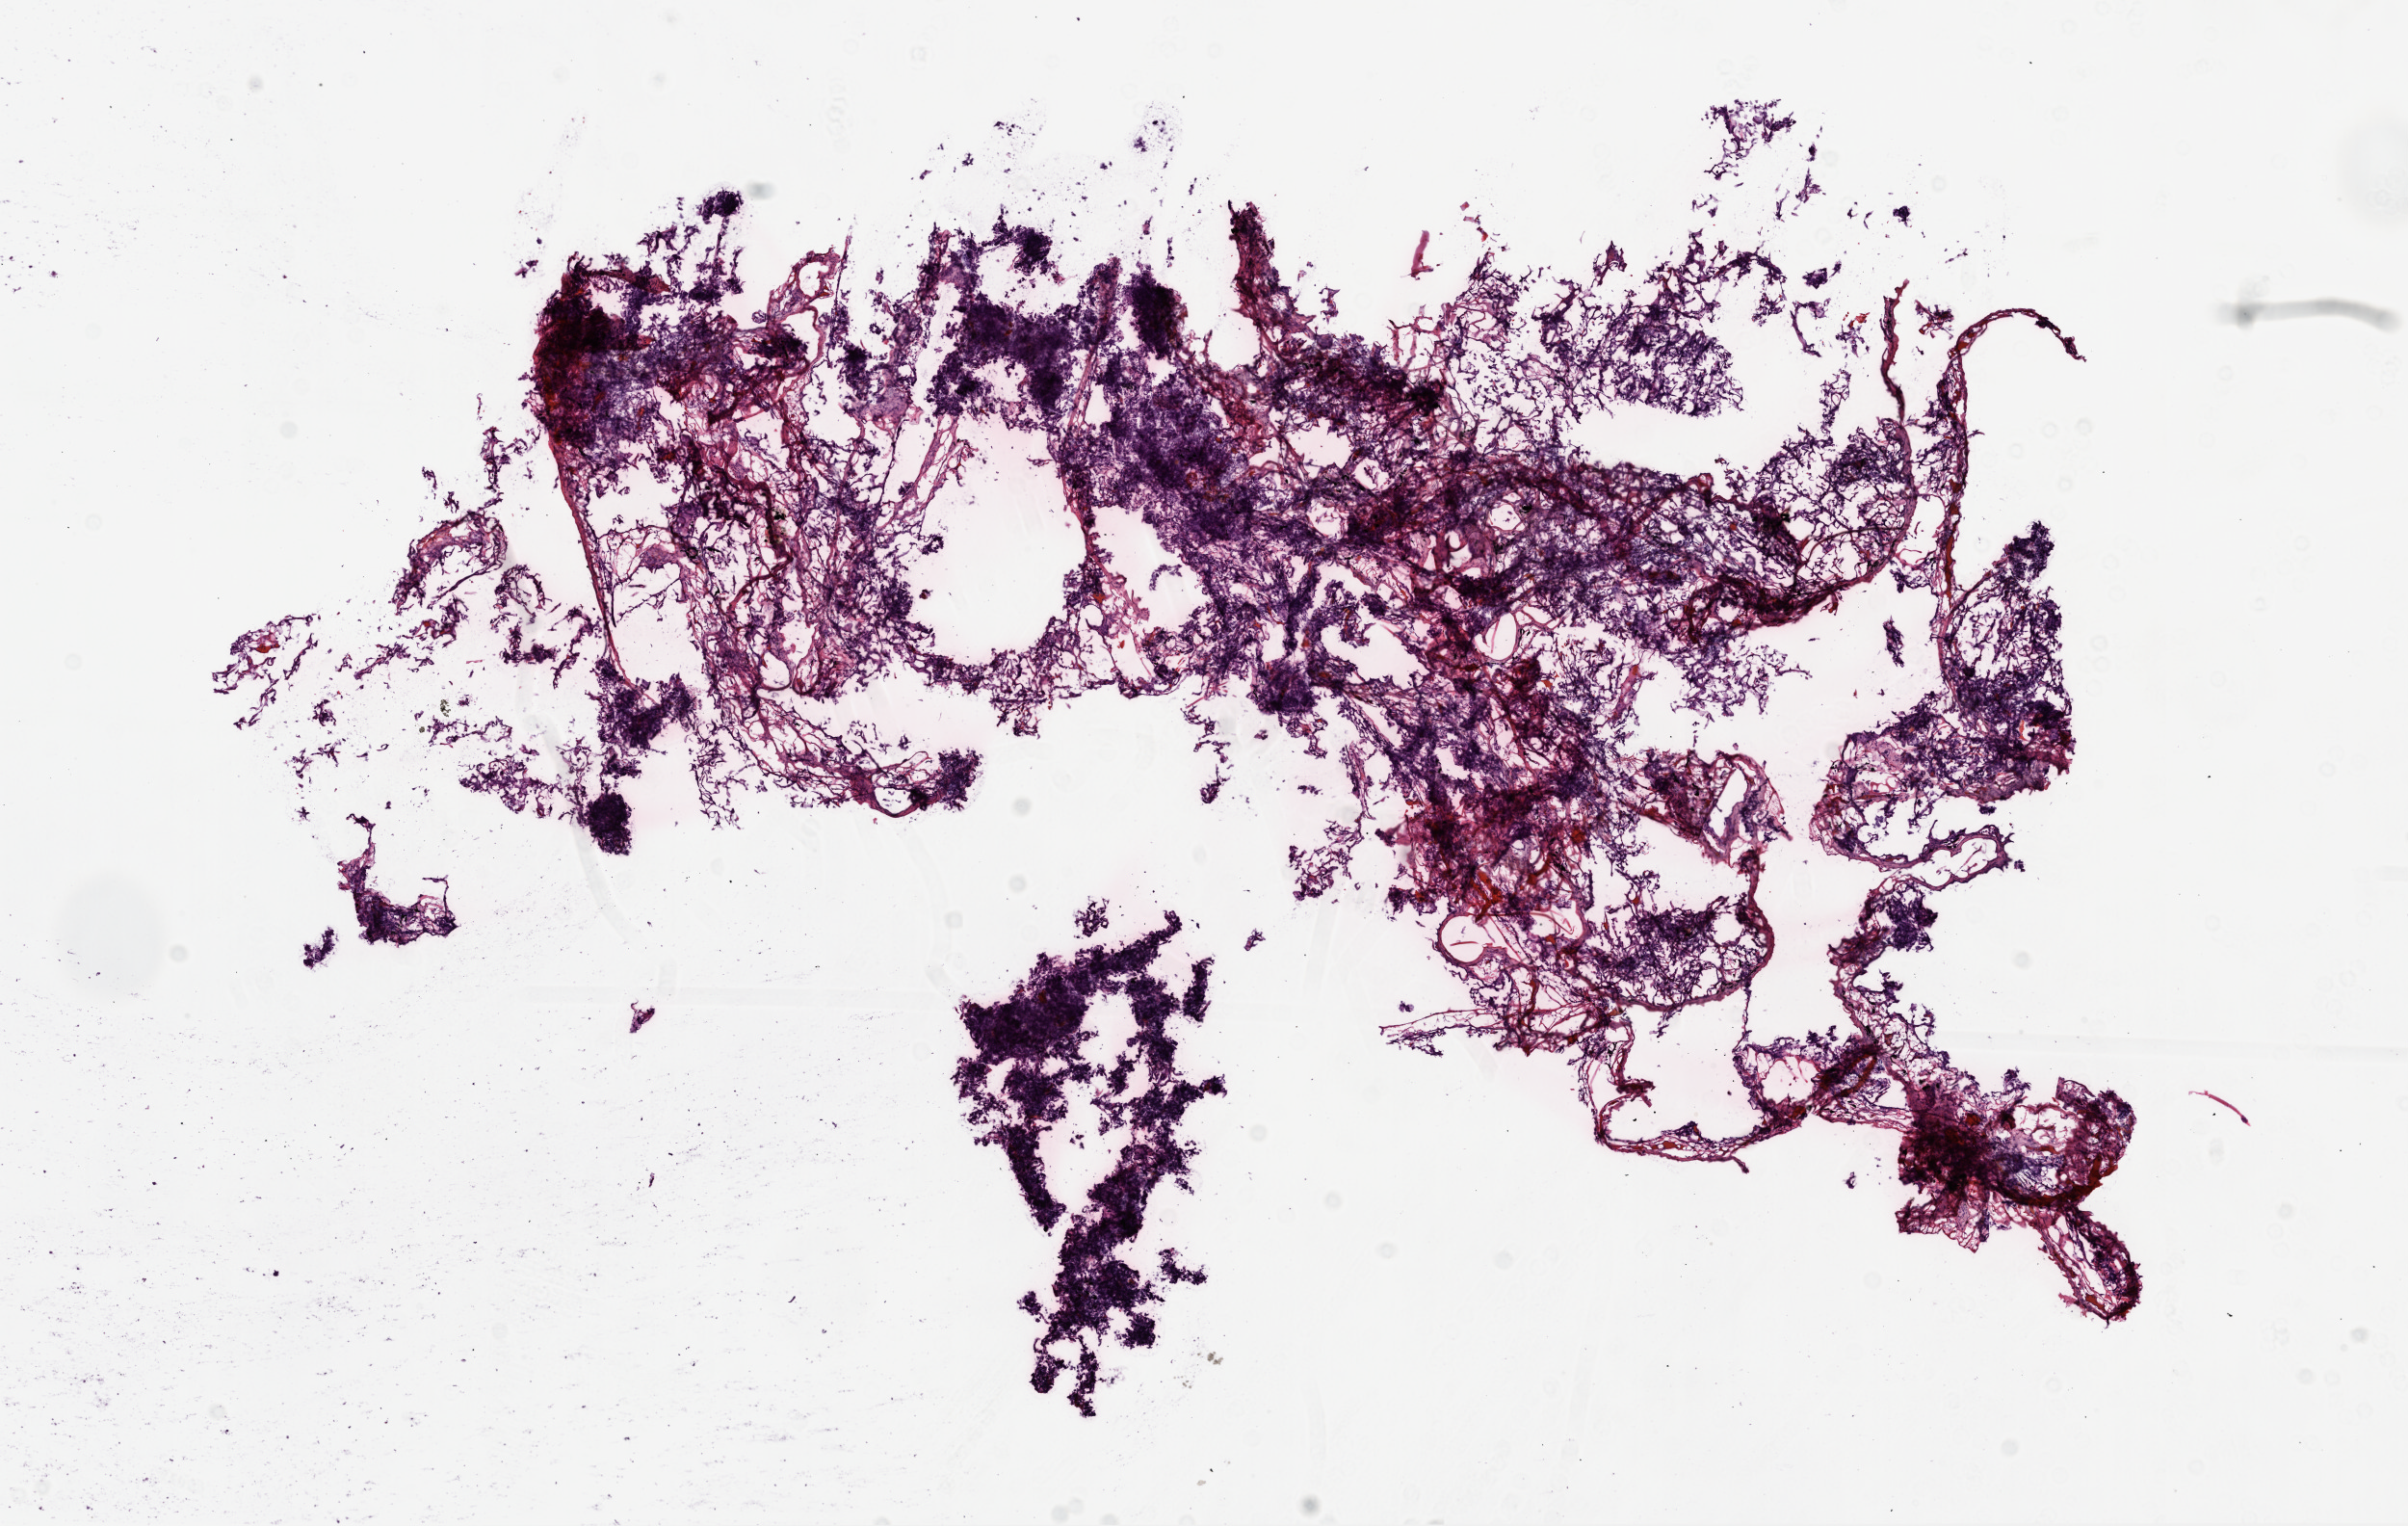
H&E whole-slide image, low-resolution overview of the scanned area, about 10.0 x 6.4 mm (slide scanned at 20x). Frozen section from the top of the tissue portion. Solid tissue normal (non-tumour tissue) sample from the lung. Male, age 39 years at initial diagnosis.
This section: solid tissue normal sample (biorepository sample class). Patient diagnosis: Squamous cell carcinoma, NOS.